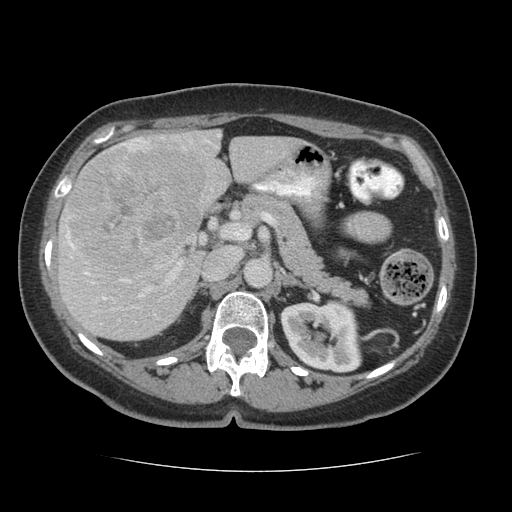
Contrast-enhanced abdominal CT (liver protocol), one axial slice. Position 33 of 75 along the scan axis. 140 kVp. Soft-tissue window (W 400 / L 40 HU). 2.5 mm slice thickness. 512 × 512 image matrix, field of view 360 × 360 mm. From the clinical record (not read from this slice): diagnosis: hepatocellular carcinoma (patient treated with transarterial chemoembolisation; whether this scan precedes or follows treatment is not stated here); TNM stage (as recorded): Stage-I; Child-Pugh class: A; tumour nodularity: uninodular.
Structures marked on this image (semi-automatically segmented with operator editing):
- liver parenchyma outside the tumour (the mass and vessels are separate outlines, so this box may not span the whole liver): box from (x=58, y=129) to (x=300, y=340) px
- mass: (x=65, y=147)–(x=205, y=287)
- liver vessels: (x=65, y=134)–(x=221, y=312)